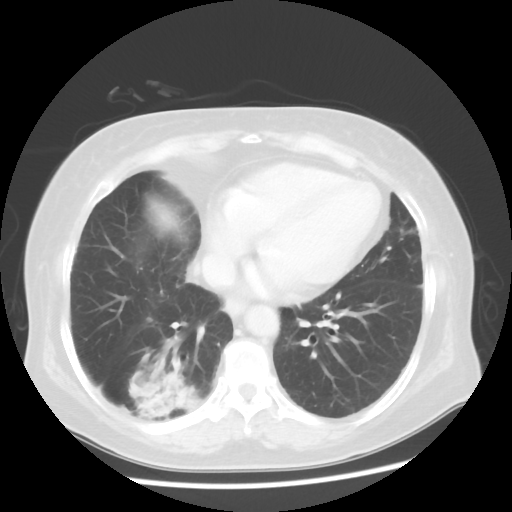
Chest CT, one axial slice; reconstruction kernel STANDARD; lung window (W 1500 / L -600 HU); 5 mm slice thickness; 512 × 512 image matrix, field of view 360 × 360 mm. Patient: female, 64 years. Case-level facts recorded for this patient, not image findings: clinical TNM (as recorded): Tis N0 M0.
Annotated regions visible in this slice (bounding box drawn by a radiologist):
- lung tumour (recorded histology: adenocarcinoma): bounding box (x1, y1, x2, y2) in pixels: (125, 357, 210, 433)